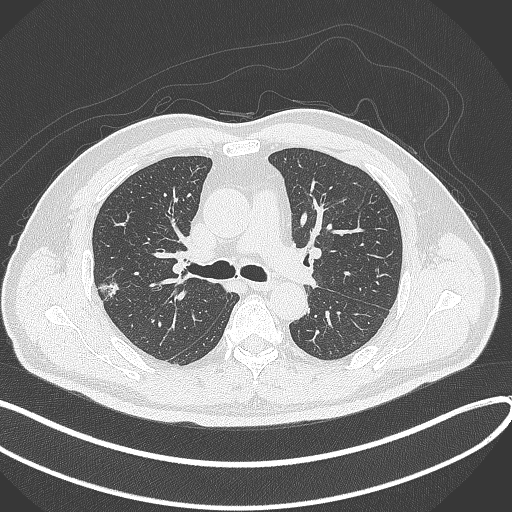
Chest CT, one axial slice. Position 215 of 372 along the scan axis. Reconstruction kernel B70f. 120 kVp. Lung window (W 1500 / L -600 HU). 512 × 512 image matrix, field of view 400 × 400 mm. Male patient, age 60 years. From the clinical record (not read from this slice): clinical TNM (as recorded): T1c N0 M0.
Annotated regions visible in this slice (bounding box drawn by a radiologist):
- lung tumour (recorded histology: adenocarcinoma): bounding box [x1, y1, x2, y2] px = [96, 271, 123, 308]